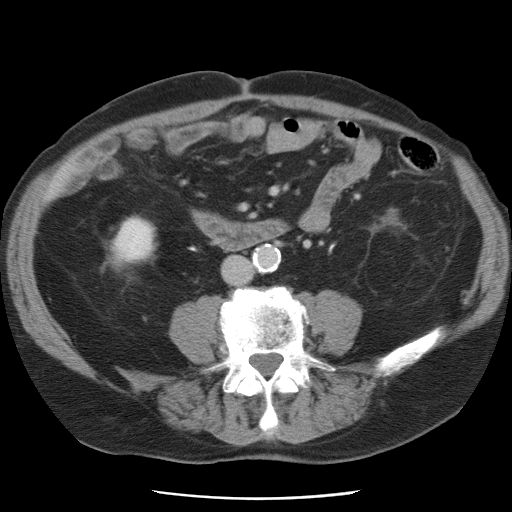
Contrast-enhanced abdominal CT, one axial slice; intravenous contrast given; soft-tissue window (W 400 / L 40 HU); 5 mm slice thickness; 512 × 512 image matrix, field of view 337 × 337 mm. Male patient, age 75 years. Case-level facts recorded for this patient, not image findings: diagnosis: colorectal cancer liver metastases, imaged before liver resection; multiple liver metastases: yes; largest metastasis: 2.4 cm; chemotherapy before resection: yes.
Outlined on this slice (manually delineated by an expert):
- liver: bounding box <50,174,65,195> (left, top, right, bottom; pixels)
- planned liver remnant (the part of the liver to remain after resection): <50,174,65,194>